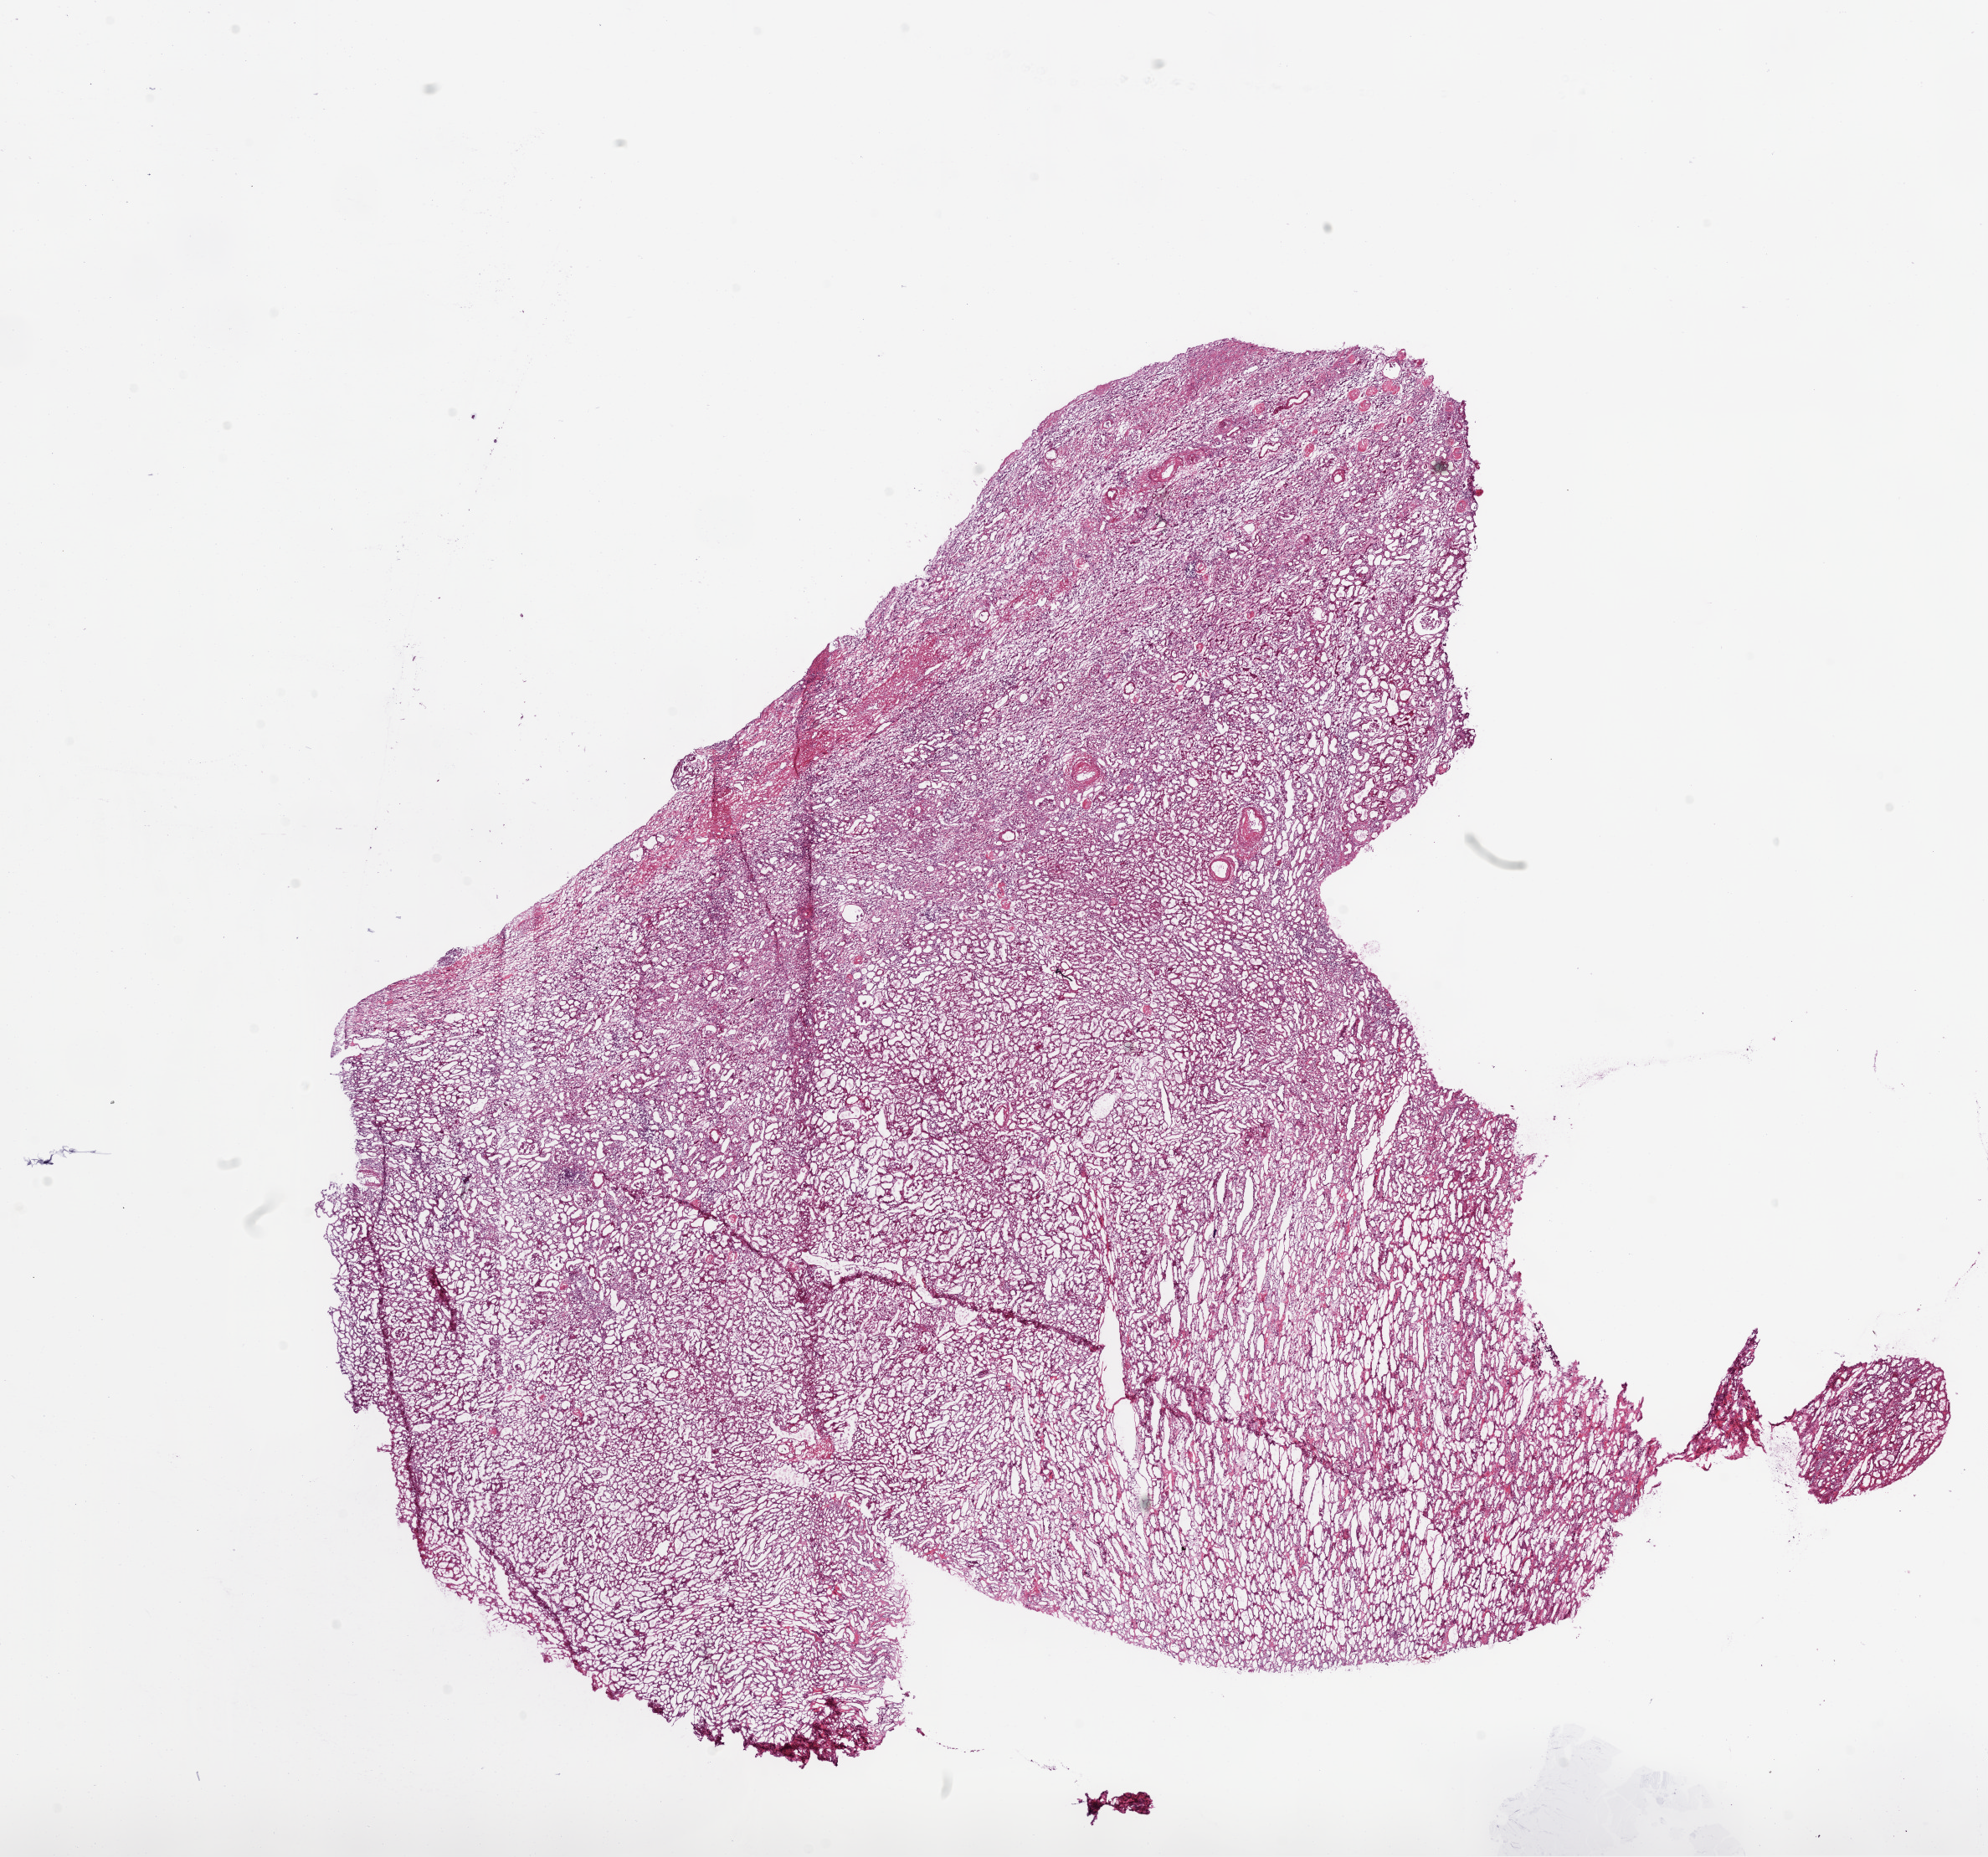
H&E-stained whole-slide image, low-resolution overview of the scanned area, about 19.1 x 17.8 mm, frozen section, kidney, solid tissue normal (non-tumour tissue) sample. Female, age 60 years at initial diagnosis.
This section: solid tissue normal (non-tumour) sample from the same patient. Patient diagnosis: Clear cell adenocarcinoma, NOS.